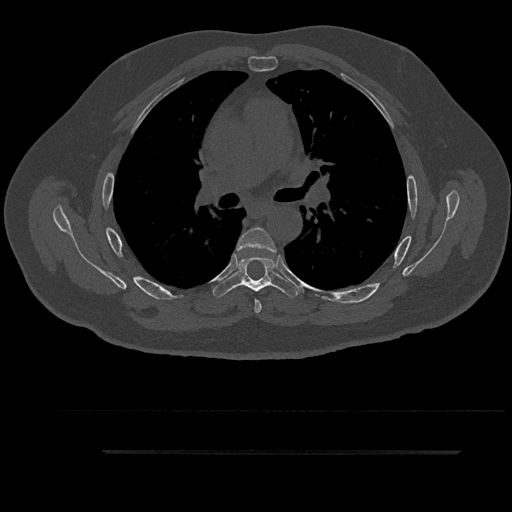
CT including the spine, one axial slice; position 597 of 797 along the scan axis; reconstruction kernel Br40s/3; 120 kVp; bone window (W 1800 / L 400 HU); 0.5 mm slice thickness; 512 × 512 image matrix. Patient: male, 63 years. Case-level facts recorded for this patient, not image findings: primary cancer: renal; vertebrae with lytic lesions (as recorded): T8.
Annotated regions visible in this slice (semi-automatically segmented with operator editing):
- T5 vertebra: bounding box <236,227,276,314> (left, top, right, bottom; pixels)
- T6 vertebra: <212,256,299,298>